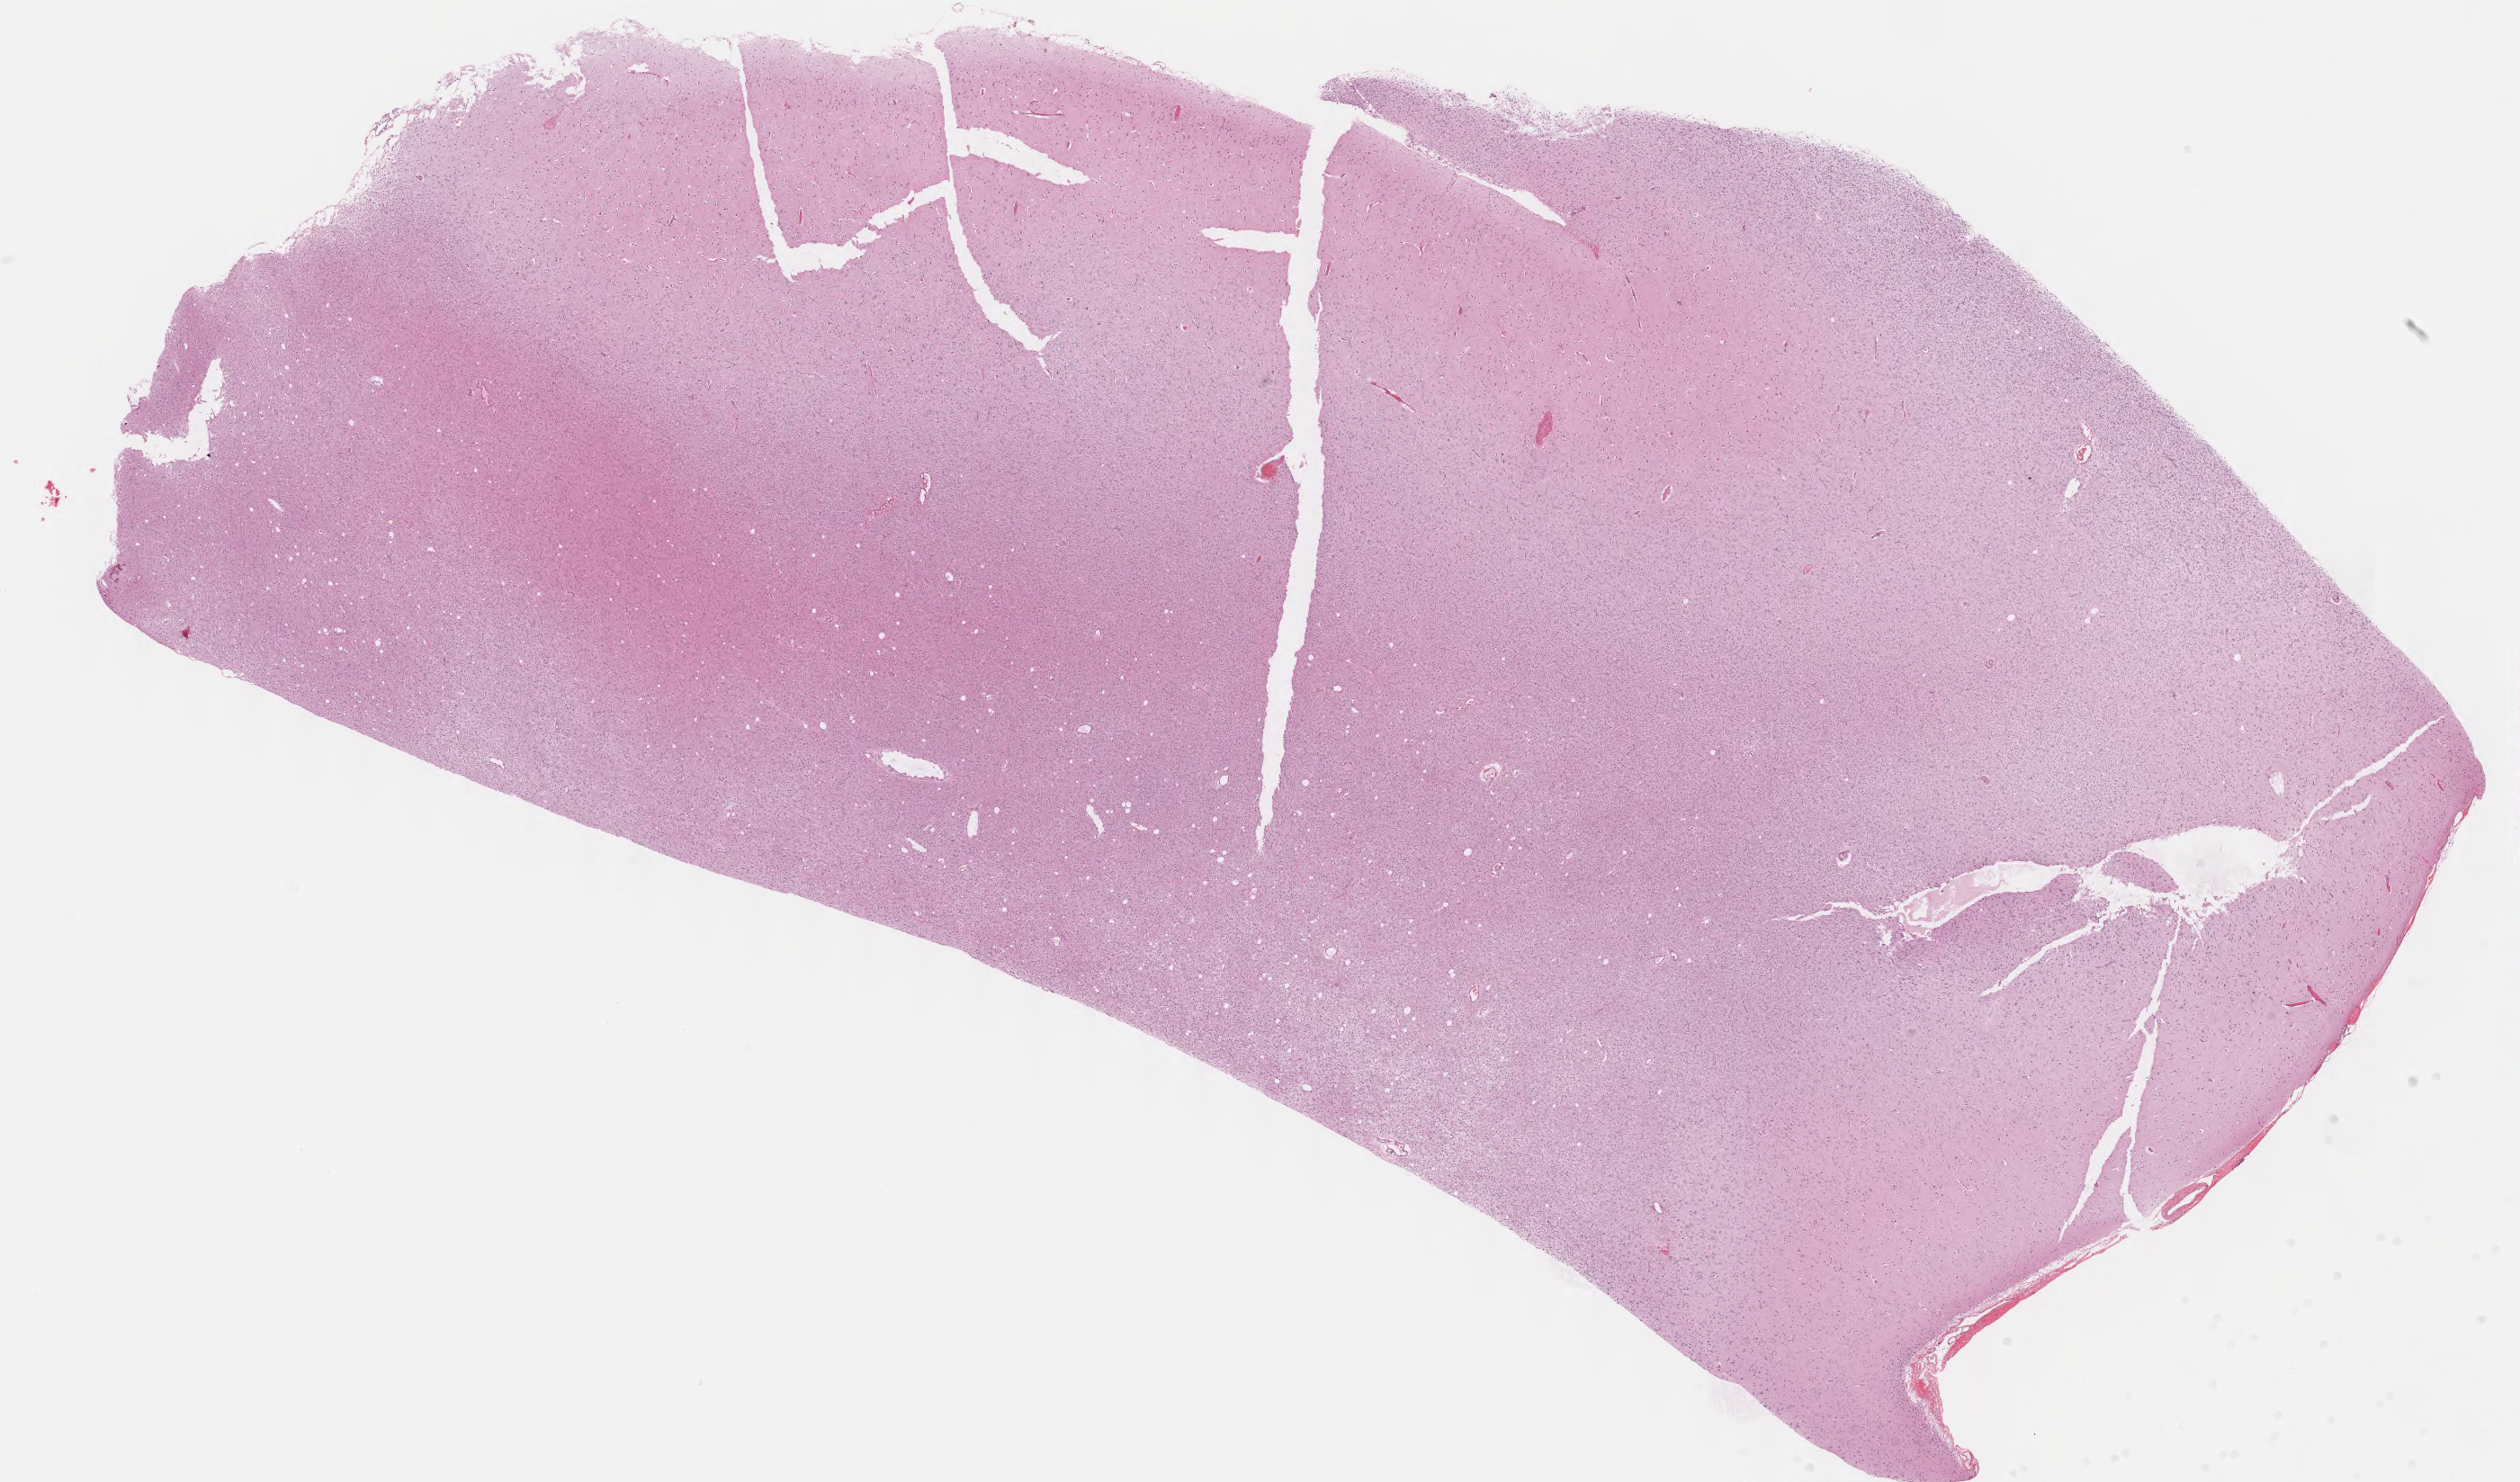
Hematoxylin and eosin (H&E) stained whole-slide image — a low-resolution overview of the entire scanned area, about 22.1 x 13.0 mm; formalin-fixed paraffin-embedded (FFPE) diagnostic section; brain, primary tumour sample. Female, age 24 years at initial diagnosis. Histologic grade: G2 (moderately differentiated).
Histologic diagnosis: Oligodendroglioma, NOS (cerebrum).